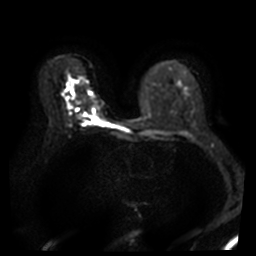
Breast MRI, one axial slice; slice 23 of 46 in the series (ordered by position); diffusion-weighted series; image 2 of 4 stored at this slice position (different b-values; order by instance number); 3 T; 5 mm slice thickness; 256 × 256 image matrix, field of view 340 × 340 mm. Female patient.
Annotated regions visible in this slice (outlined manually by an expert reader):
- tumour on diffusion-weighted imaging: bounding box [x1, y1, x2, y2] px = [93, 117, 98, 120]